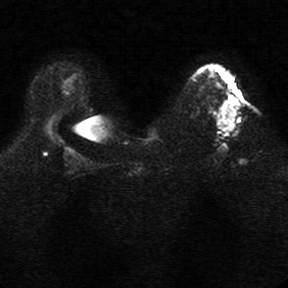
Breast MRI, one axial slice; slice 17 of 34 in the series (ordered by position); diffusion-weighted series; image 2 of 4 stored at this slice position (different b-values; order by instance number); 1.5 T; 288 × 288 image matrix. Female patient.
Outlined on this slice (manually delineated by an expert):
- tumour on diffusion-weighted imaging: bounding box [x1, y1, x2, y2] px = [221, 96, 238, 132]